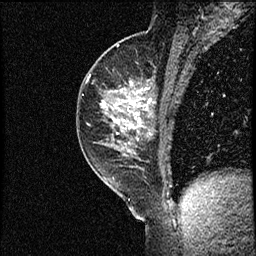
Breast MRI (dynamic contrast-enhanced), one sagittal slice; position 34 of 56 along the scan axis; dynamic contrast-enhanced study with each time point stored as its own series, time point 2 of 3 at this slice position (early post-contrast, ordered by acquisition time); 1.5 T; TE 4.2 ms, TR 17.3 ms; 2 mm slice thickness; 256 × 256 image matrix, field of view 200 × 200 mm. Female patient. Case-level facts recorded for this patient, not image findings: setting: breast cancer imaged before/during neoadjuvant chemotherapy; receptor status: HER2-positive.
Outlined on this slice (semi-automatically segmented with operator editing):
- analysis volume of interest (the breast-tissue region the enhancement analysis was run in; not a lesion): box from (x=76, y=50) to (x=156, y=155) px
- tumour enhancement mask (voxels above the 100 % enhancement threshold inside the analysis volume of interest): (x=112, y=81)–(x=152, y=130)